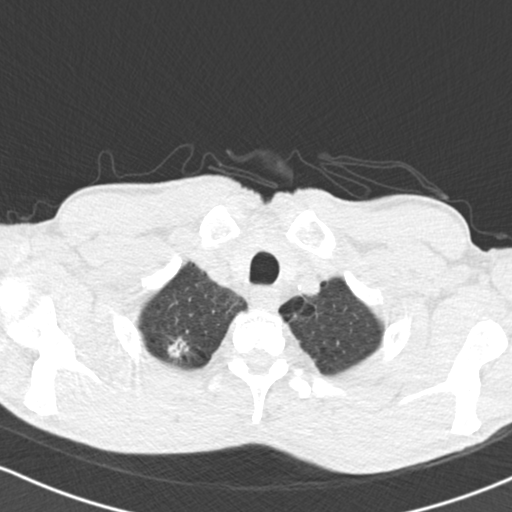
Chest CT (low-dose screening protocol), one axial image; first (baseline) screen; lung window (W 1500 / L -600 HU); 2 mm slice thickness; 120 kVp; slice 24 of 151 in the series. Male, age 64 years at enrolment. Current smoker at enrolment.
Lesion marked by an expert reader, bounding box (x1, y1, x2, y2) in pixels: (148, 324, 201, 376). The exam's reader record, not a measurement of the box and not confirmed to be the same lesion: non-calcified nodule or mass ≥4 mm, right upper lobe, 13 × 11 mm, spiculated (stellate) margins, soft tissue attenuation. Official screen result: positive, change unspecified: nodule(s) >= 4 mm or enlarging nodule(s), mass(es), or other non-specific abnormalities suspicious for lung cancer. Lung cancer was diagnosed 161 days after this screen: adenocarcinoma, NOS, right upper lobe, poorly differentiated (G3), stage IA (AJCC 6th edition), 13 mm at pathology.